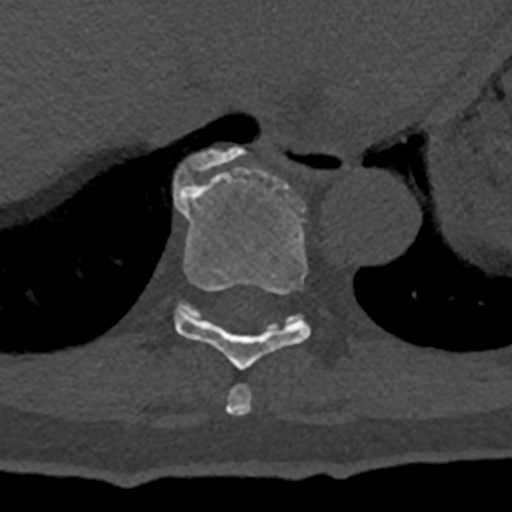
CT including the spine, one axial slice; slice 646 of 797 in the series (ordered by position); reconstruction kernel Br40s/3; 120 kVp; bone window (W 1800 / L 400 HU); 0.5 mm slice thickness; 512 × 512 image matrix, field of view 160 × 160 mm. Male patient, age 74 years. Case-level facts recorded for this patient, not image findings: primary cancer: renal; vertebrae with lytic lesions (as recorded): T10, L1, L2, L3, L4, L5.
Outlined on this slice (semi-automatic segmentation, software-assisted and operator-edited):
- T10 vertebra: bounding box [x1, y1, x2, y2] px = [174, 147, 299, 327]
- T8 vertebra: [226, 384, 252, 415]
- T9 vertebra: [174, 168, 311, 370]